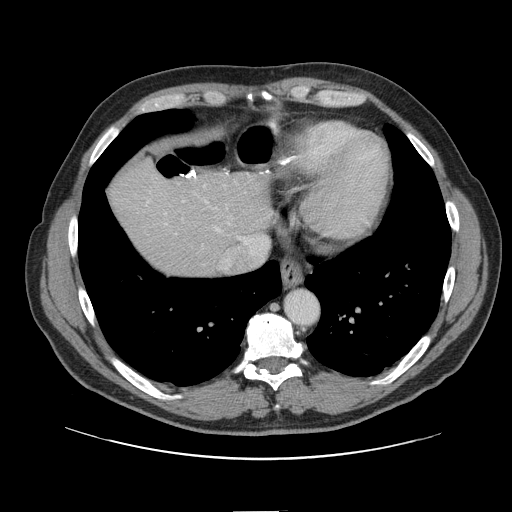
Contrast-enhanced abdominal CT, one axial slice; position 131 of 161 along the scan axis; 120 kVp; intravenous contrast given; soft-tissue window (W 400 / L 40 HU); 512 × 512 image matrix. Male patient, age 66 years. From the clinical record (not read from this slice): diagnosis: colorectal cancer liver metastases, imaged before liver resection; multiple liver metastases: no; largest metastasis: 3.5 cm.
Annotated regions visible in this slice (outlined manually by an expert reader):
- hepatic veins: bounding box <147,186,231,269> (left, top, right, bottom; pixels)
- liver: <111,161,271,277>
- planned liver remnant (the part of the liver to remain after resection): <111,161,271,275>